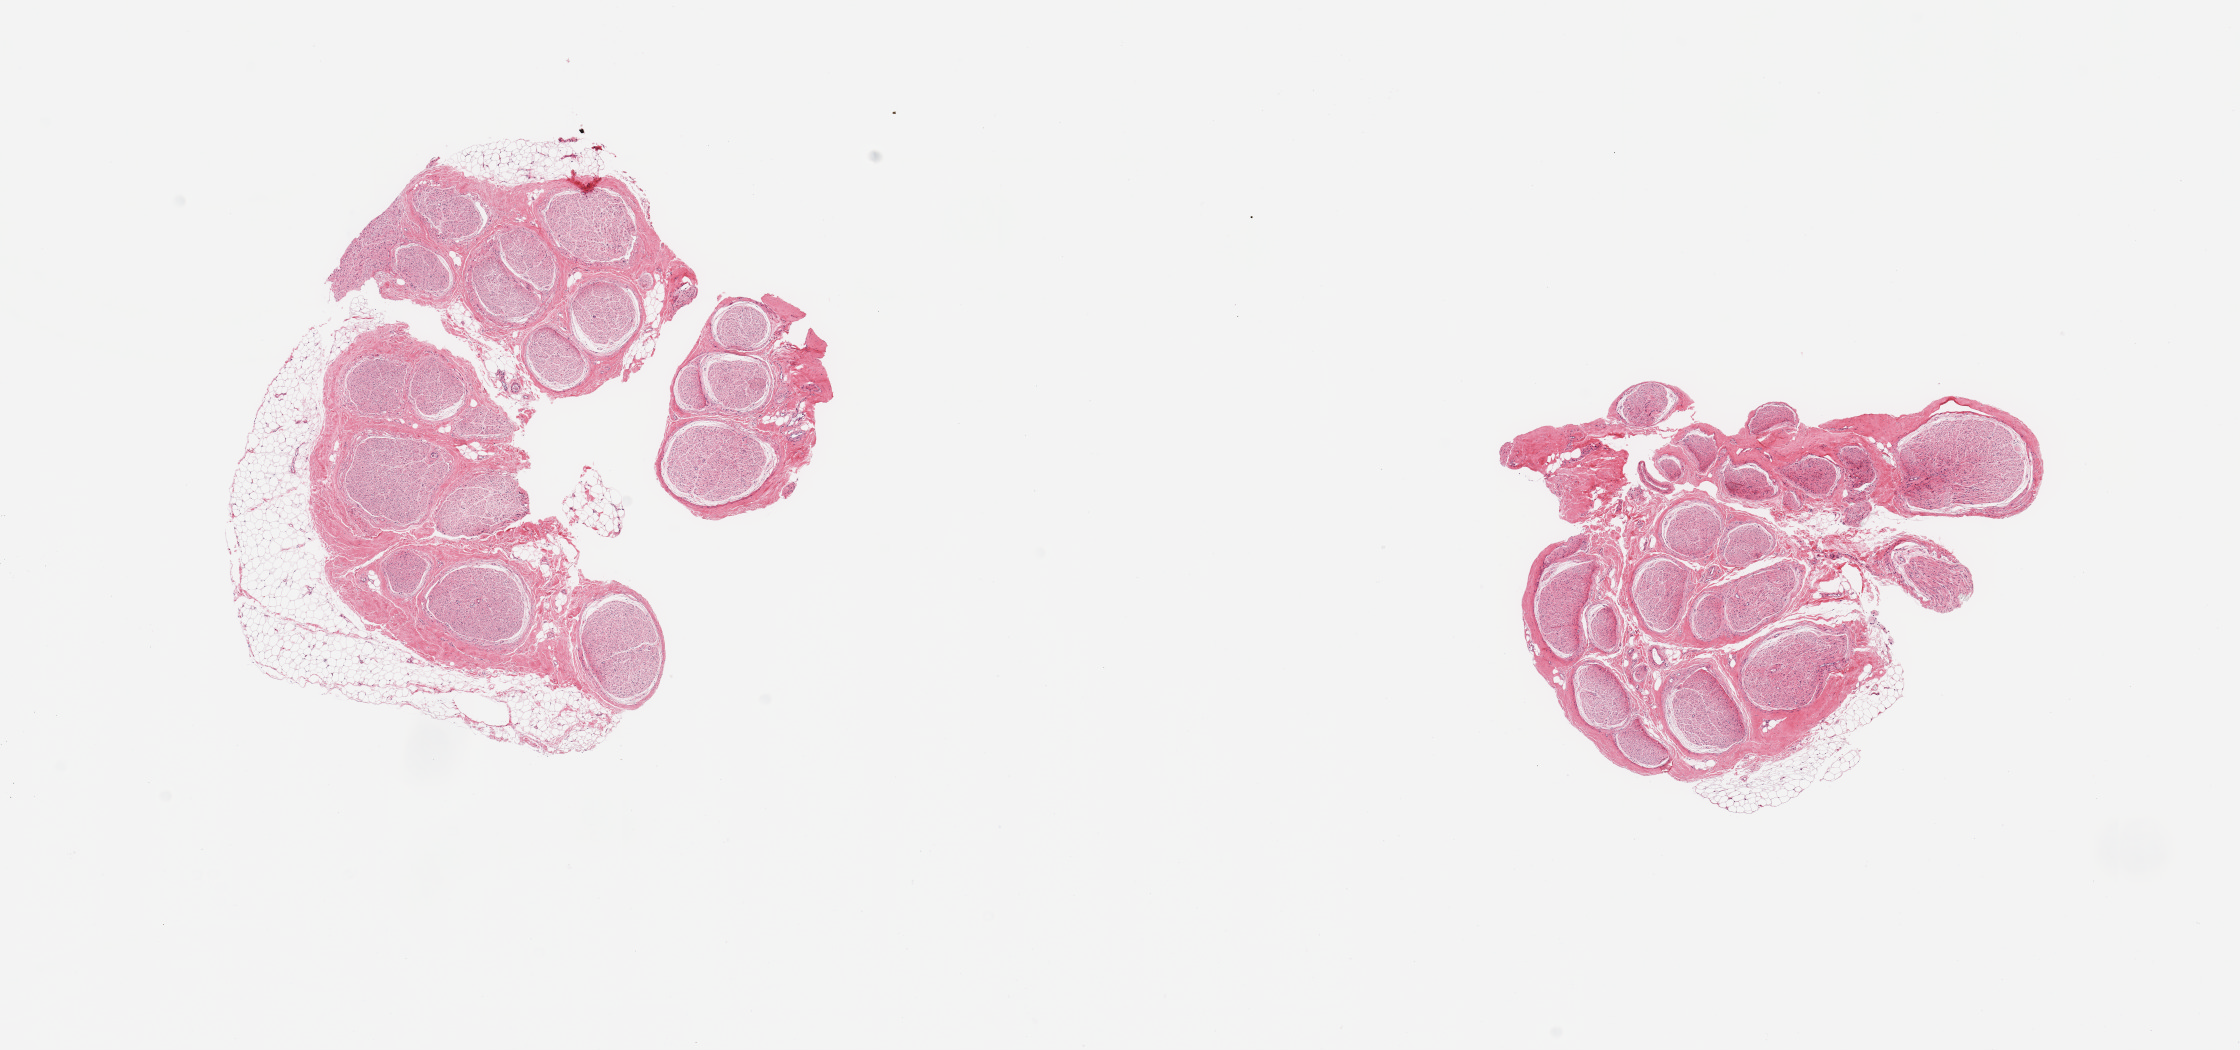
Haematoxylin and eosin whole-slide image, low-resolution overview of the scanned area, about 17.7 x 8.3 mm (acquisition: 20x scan), PAXgene-fixed paraffin-embedded (PFPE) section, sampled site (target tissue): tibial nerve, tissue donor sample.
- review note (as recorded): 2 pieces; up to 0.8mm (25%) and 0.4mm external fat